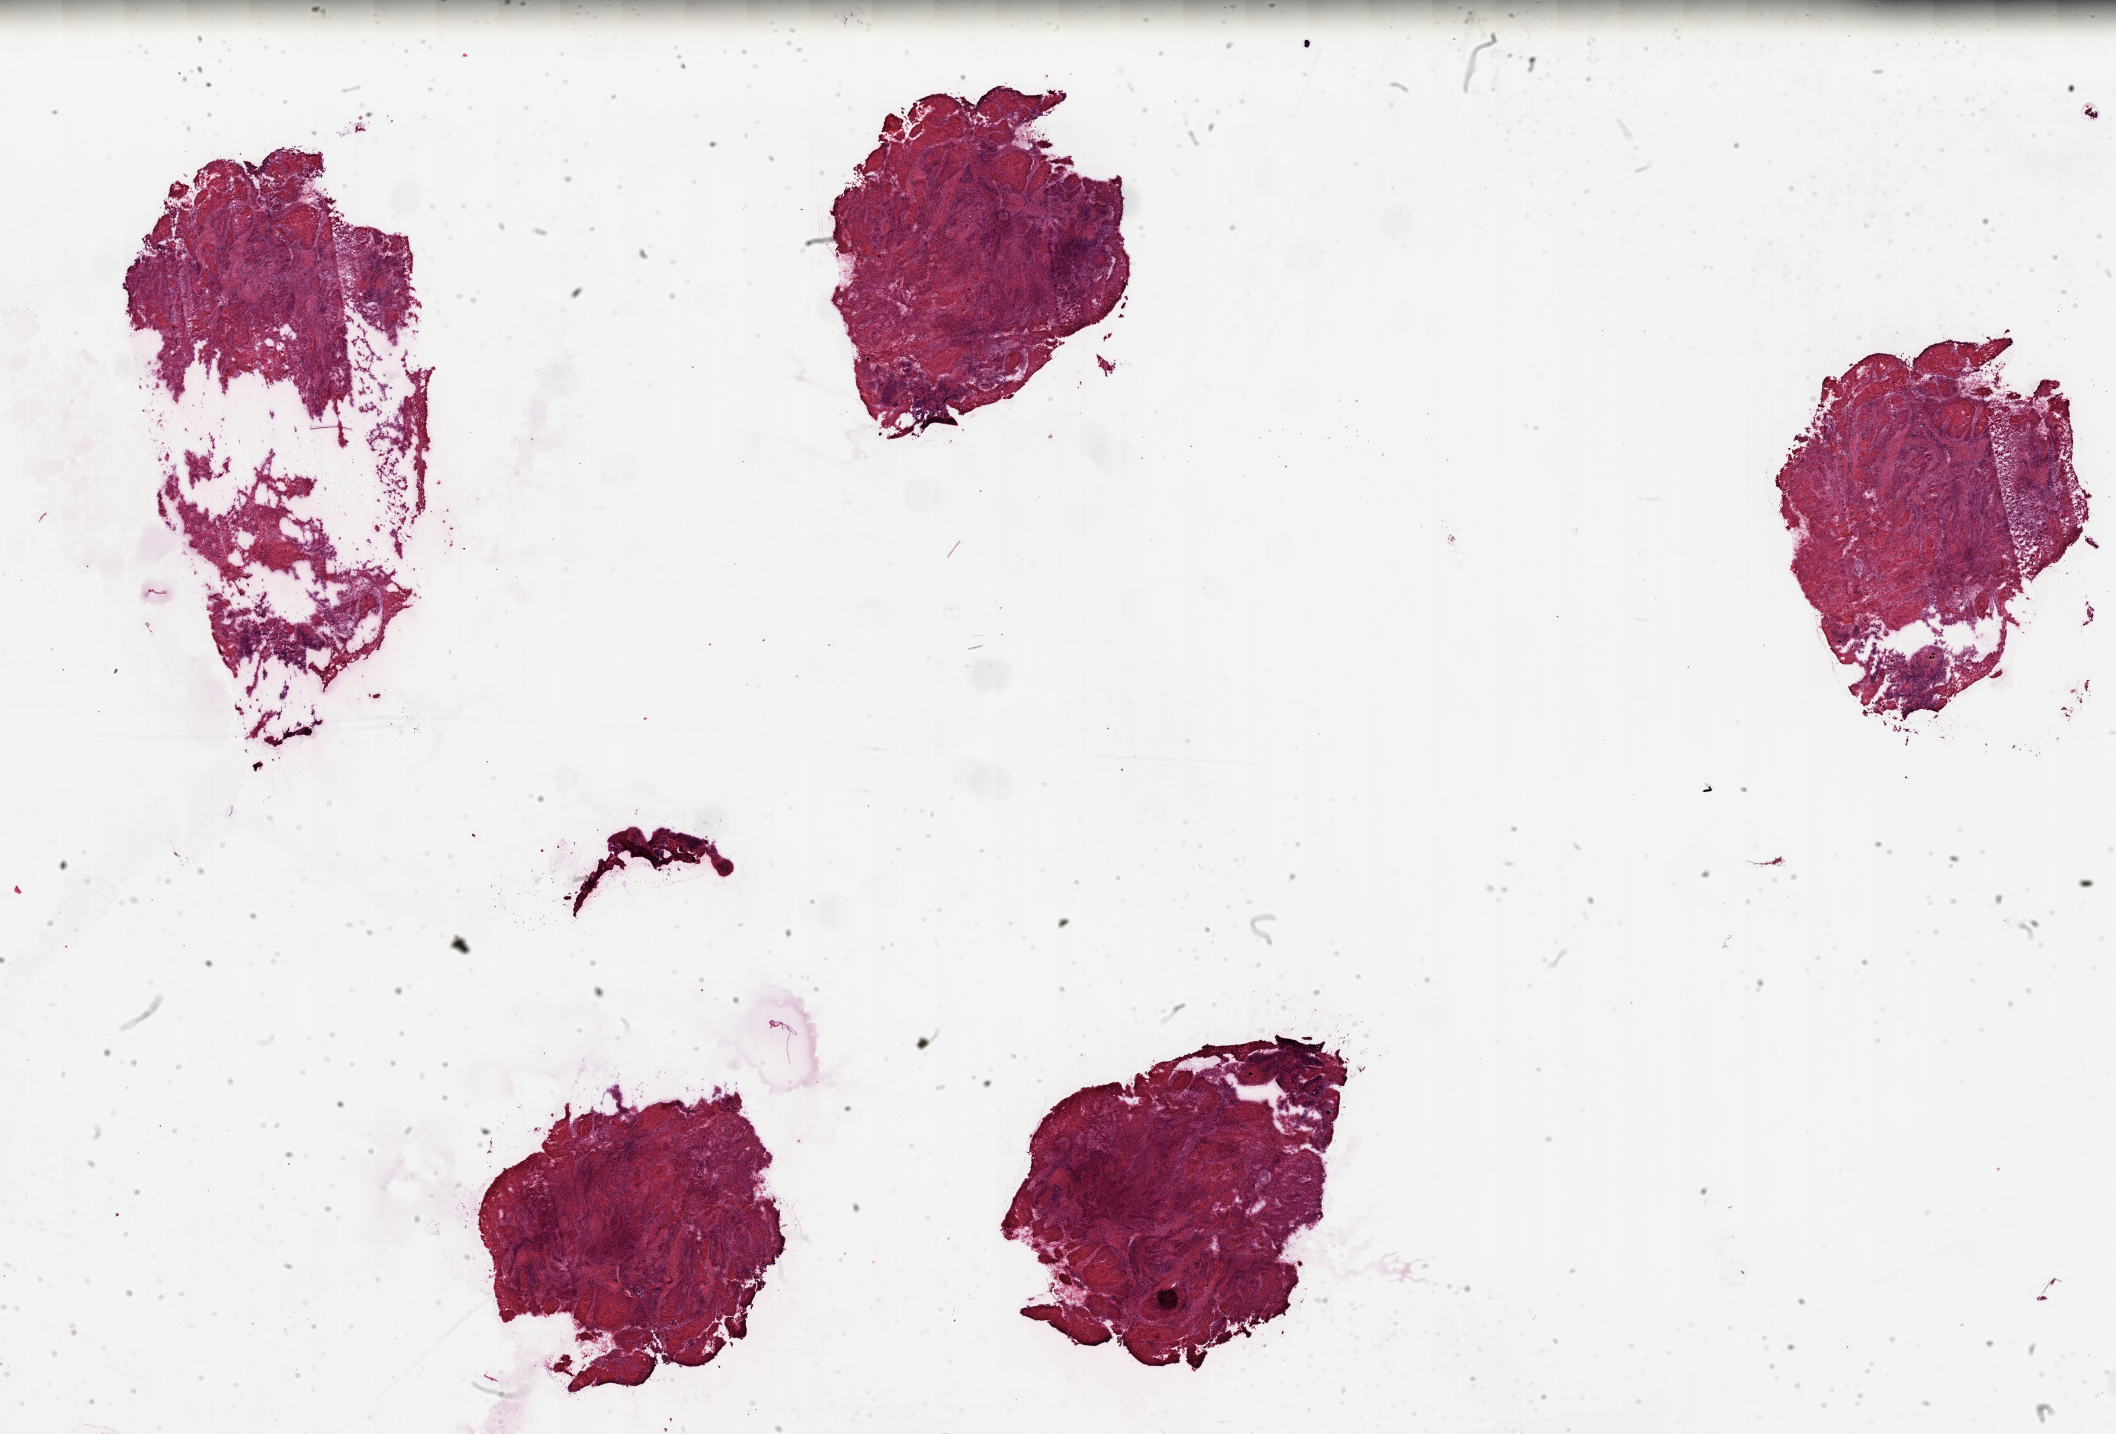
Whole-slide histology image, H&E-stained — a low-resolution overview of the entire scanned area, about 33.5 x 22.7 mm (slide scanned at 20x); head and neck, tissue type not recorded. 69-year-old male patient.
- patient diagnosis: Squamous cell carcinoma, NOS (larynx, NOS)